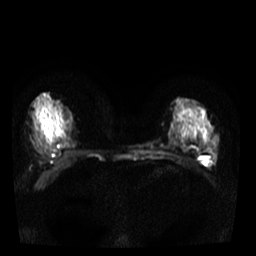
Breast MRI, one axial slice. Slice 18 of 40 in the series (ordered by position). Diffusion-weighted series; image 2 of 4 stored at this slice position (different b-values; order by instance number). 3 T. 5 mm slice thickness. 256 × 256 image matrix, field of view 320 × 320 mm. Female patient.
Outlined on this slice (outlined manually by an expert reader):
- tumour on diffusion-weighted imaging: bounding box <208,164,210,166> (left, top, right, bottom; pixels)